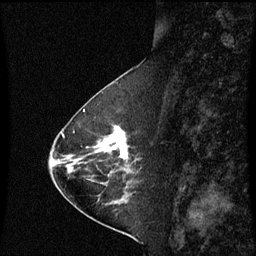
Breast MRI (dynamic contrast-enhanced), one sagittal slice; slice 24 of 60 in the series (ordered by position); dynamic contrast-enhanced series, image 2 of 3 at this slice position (ordered by acquisition); 1.5 T; TE 4.2 ms, TR 8.9 ms; 256 × 256 image matrix, field of view 200 × 200 mm. Female patient, age 63 years. From the clinical record (not read from this slice): setting: breast cancer imaged before/during neoadjuvant chemotherapy; receptor status: HR-positive, HER2-negative.
Annotated regions visible in this slice (semi-automatic segmentation, software-assisted and operator-edited):
- analysis volume of interest (the breast-tissue region the enhancement analysis was run in; not a lesion): box from (x=94, y=126) to (x=141, y=175) px
- tumour enhancement mask (voxels above the 70 % enhancement threshold inside the analysis volume of interest): (x=99, y=126)–(x=129, y=159)